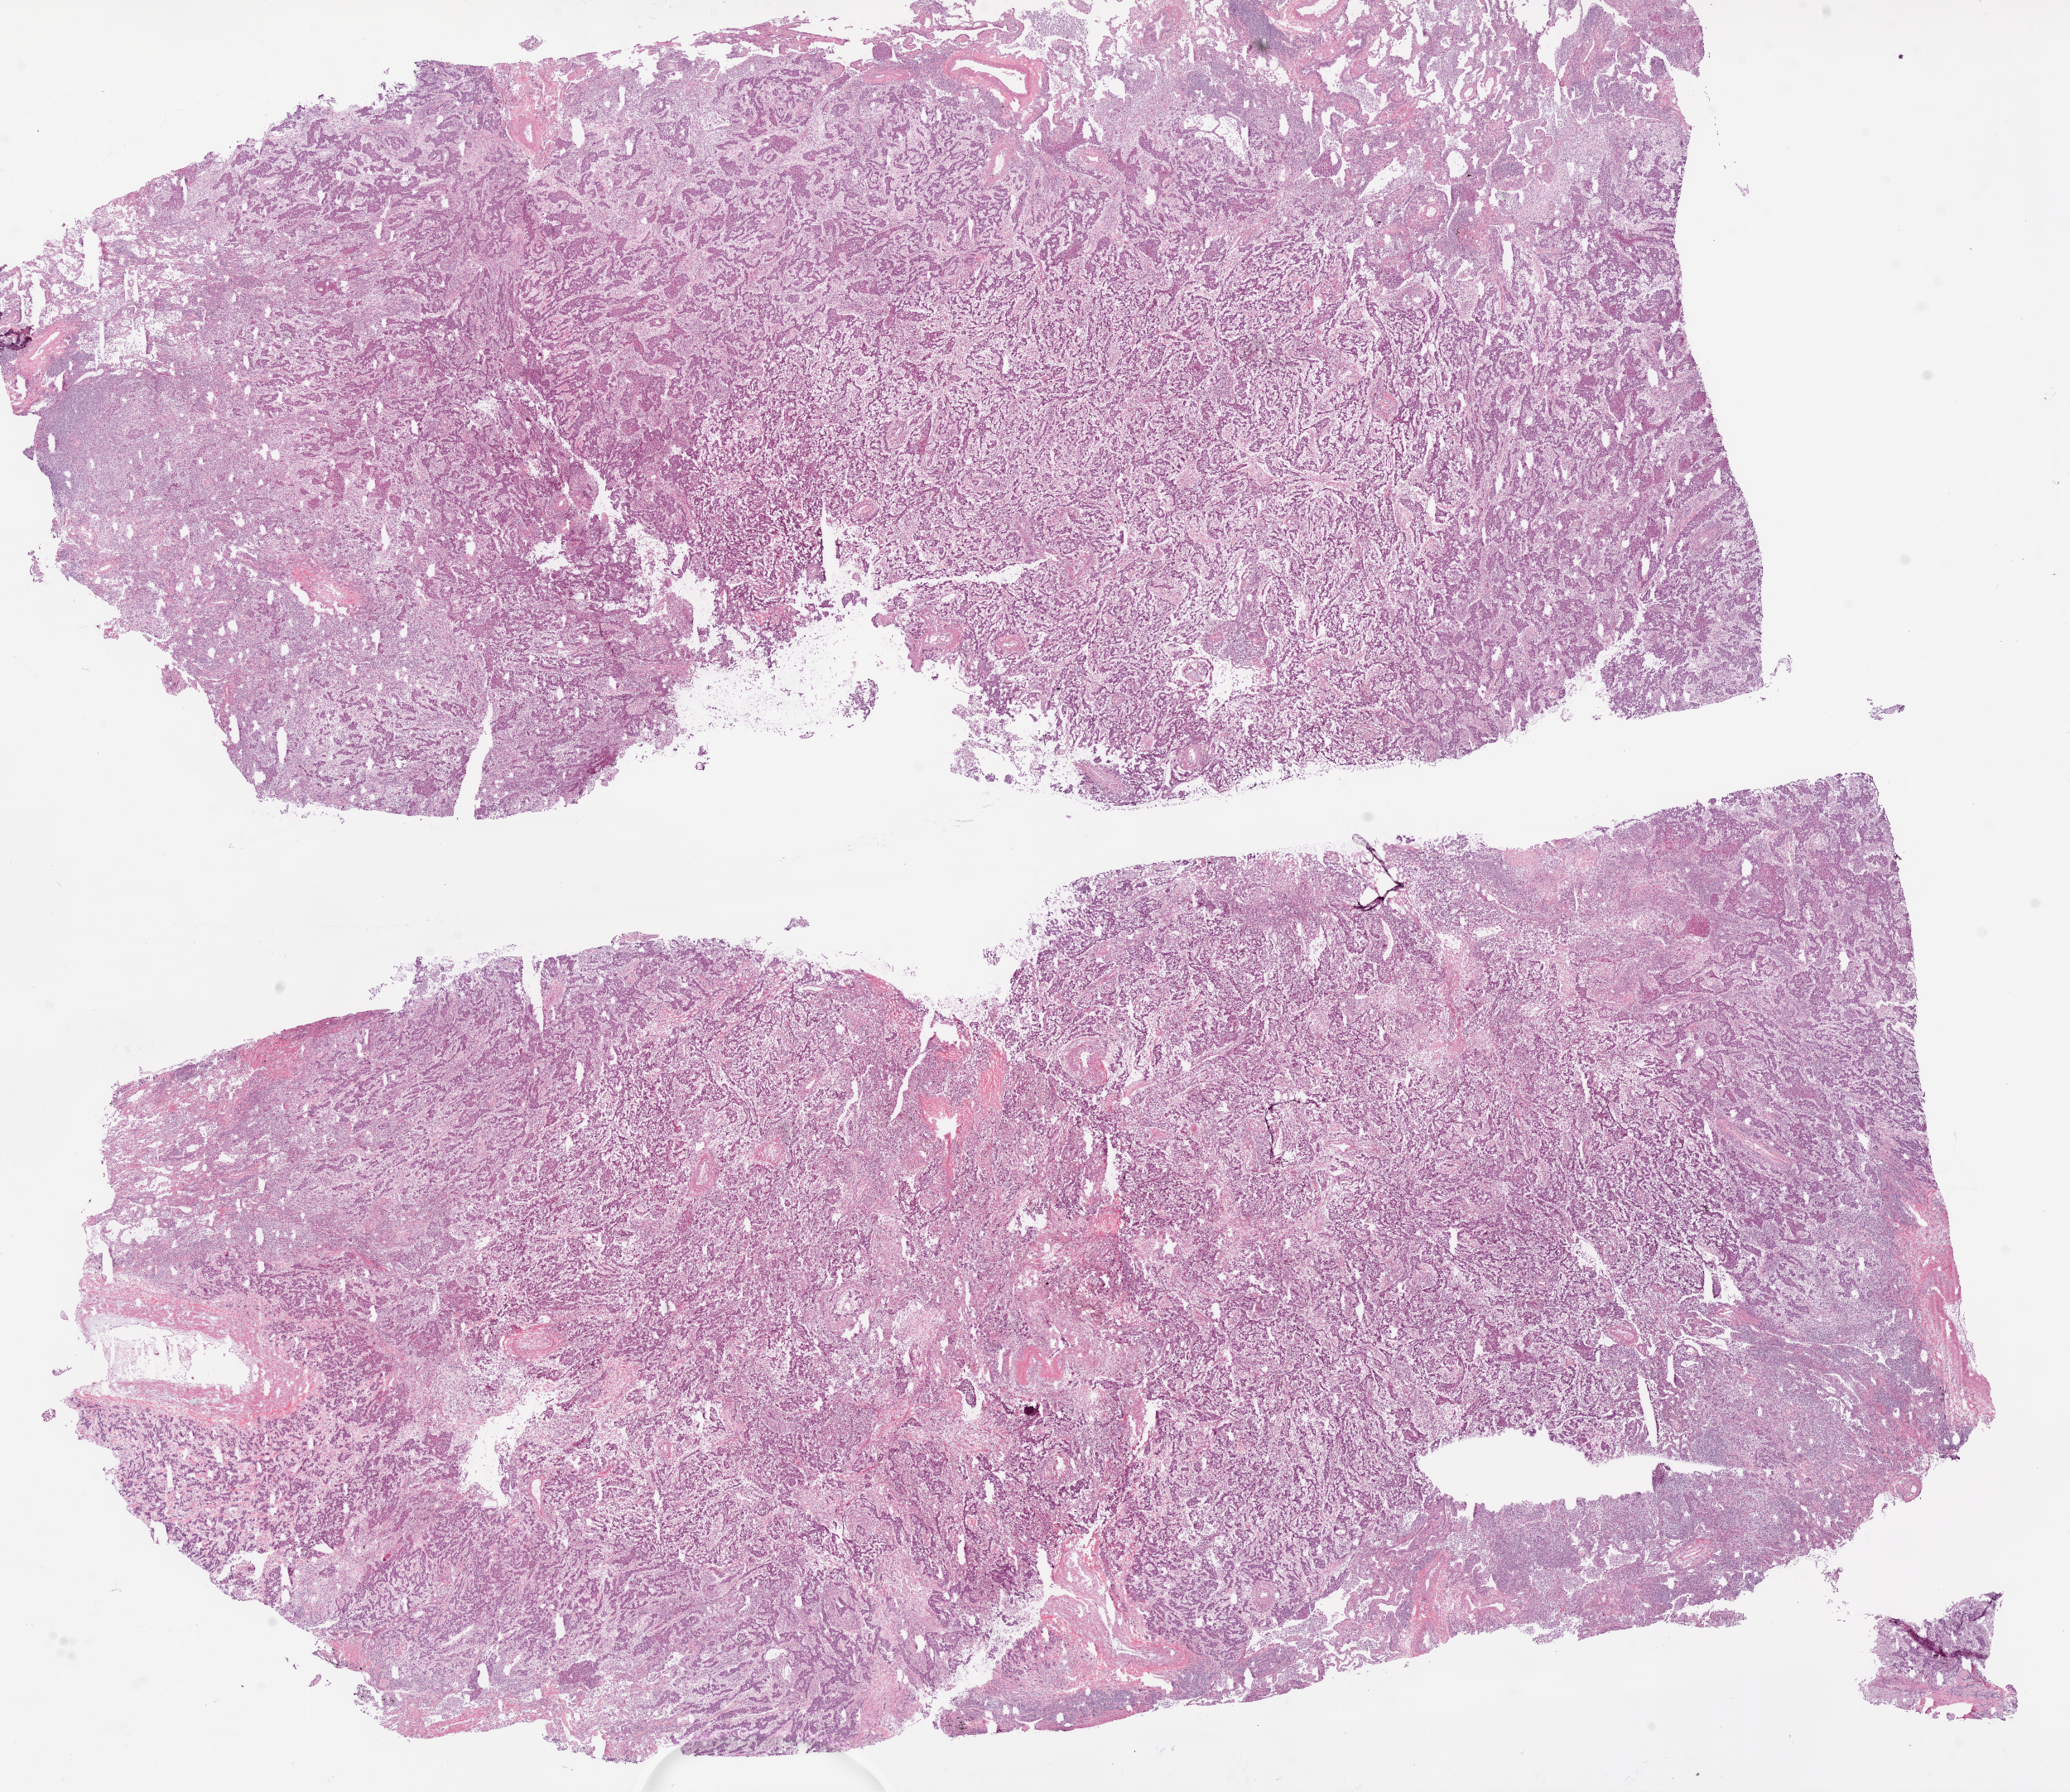
H&E whole-slide image, a low-resolution overview of the entire scanned area, about 20.1 x 17.4 mm (acquisition: 20x scan), frozen section from the bottom of the tissue portion, primary tumour sample from the lung. Patient: female, age at initial diagnosis 72 years. Pathologist review of this section (percent, as recorded): tumour cells 65%, tumour nuclei 75%, normal cells 10%, stromal cells 20%, necrosis 5%.
- laterality: right
- diagnosis: Squamous cell carcinoma, NOS (lower lobe, lung)
- AJCC pathologic stage: IA (6th edition)